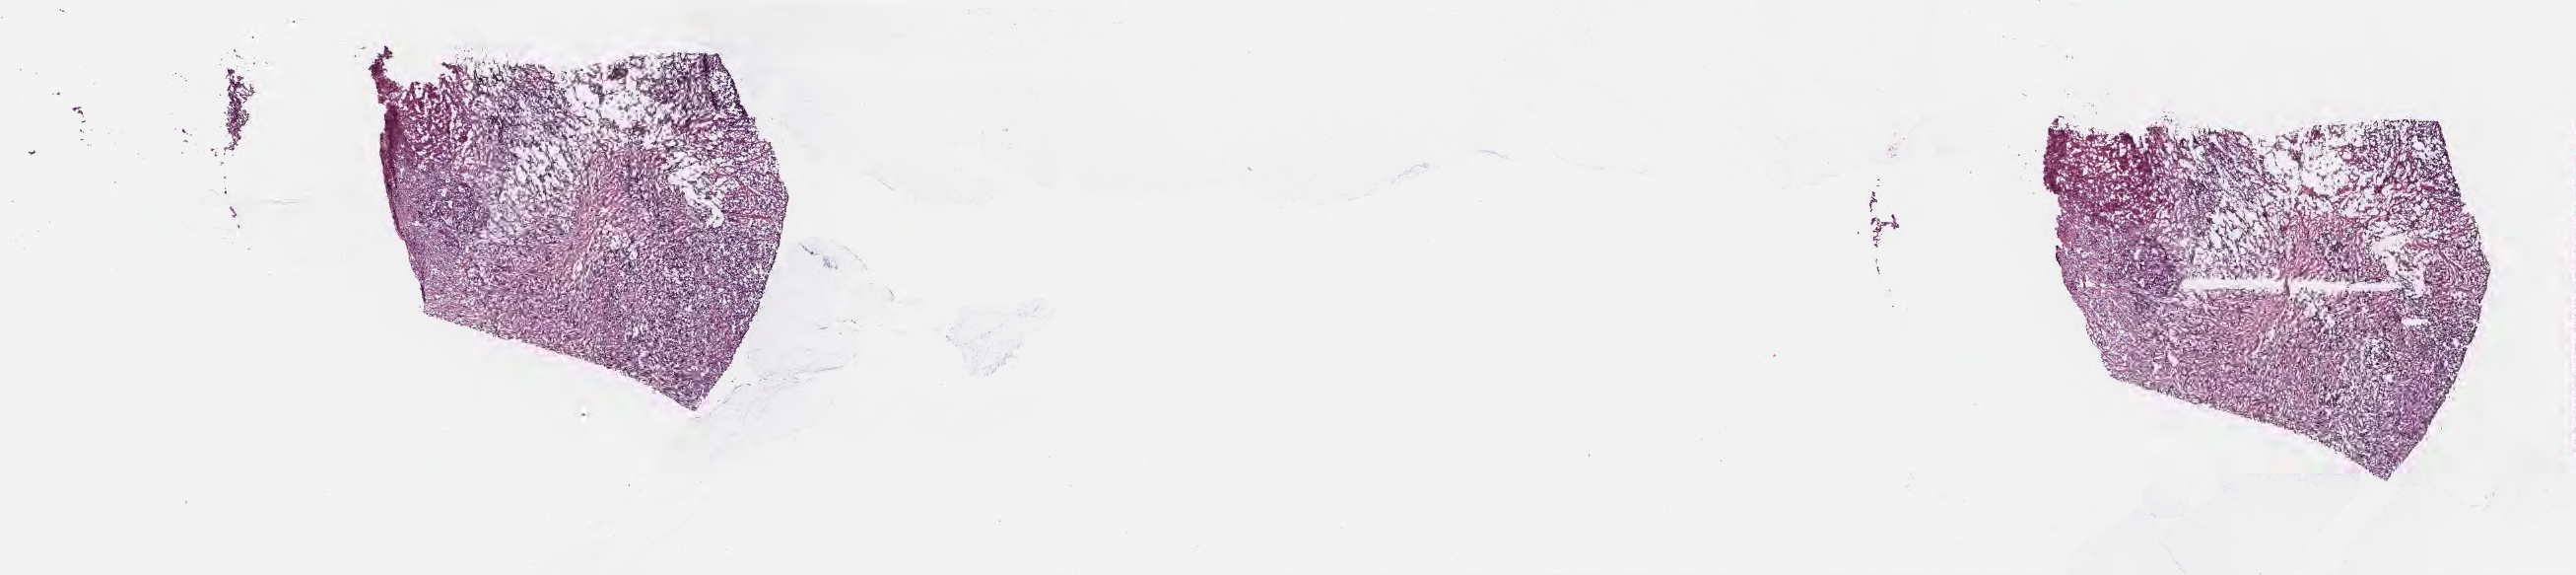
H&E whole-slide image — a low-resolution overview of the entire scanned area, about 21.1 x 4.7 mm. Frozen section (tissue freezing medium). Primary tumor. Anatomic site: tail of pancreas. Female patient; age at initial diagnosis 71 years. Tumor grade: G3 (poorly differentiated). Composition of this section per pathologist review: tumor cells 40%, tumor nuclei 50%, stromal cells 60%, necrosis 0%, normal cells 0%. Infiltration values recorded for this section: lymphocyte infiltration 0%, monocyte infiltration 0%, neutrophil infiltration 0%.
- AJCC pathologic stage: Stage IA
- diagnosis: Infiltrating duct carcinoma, NOS